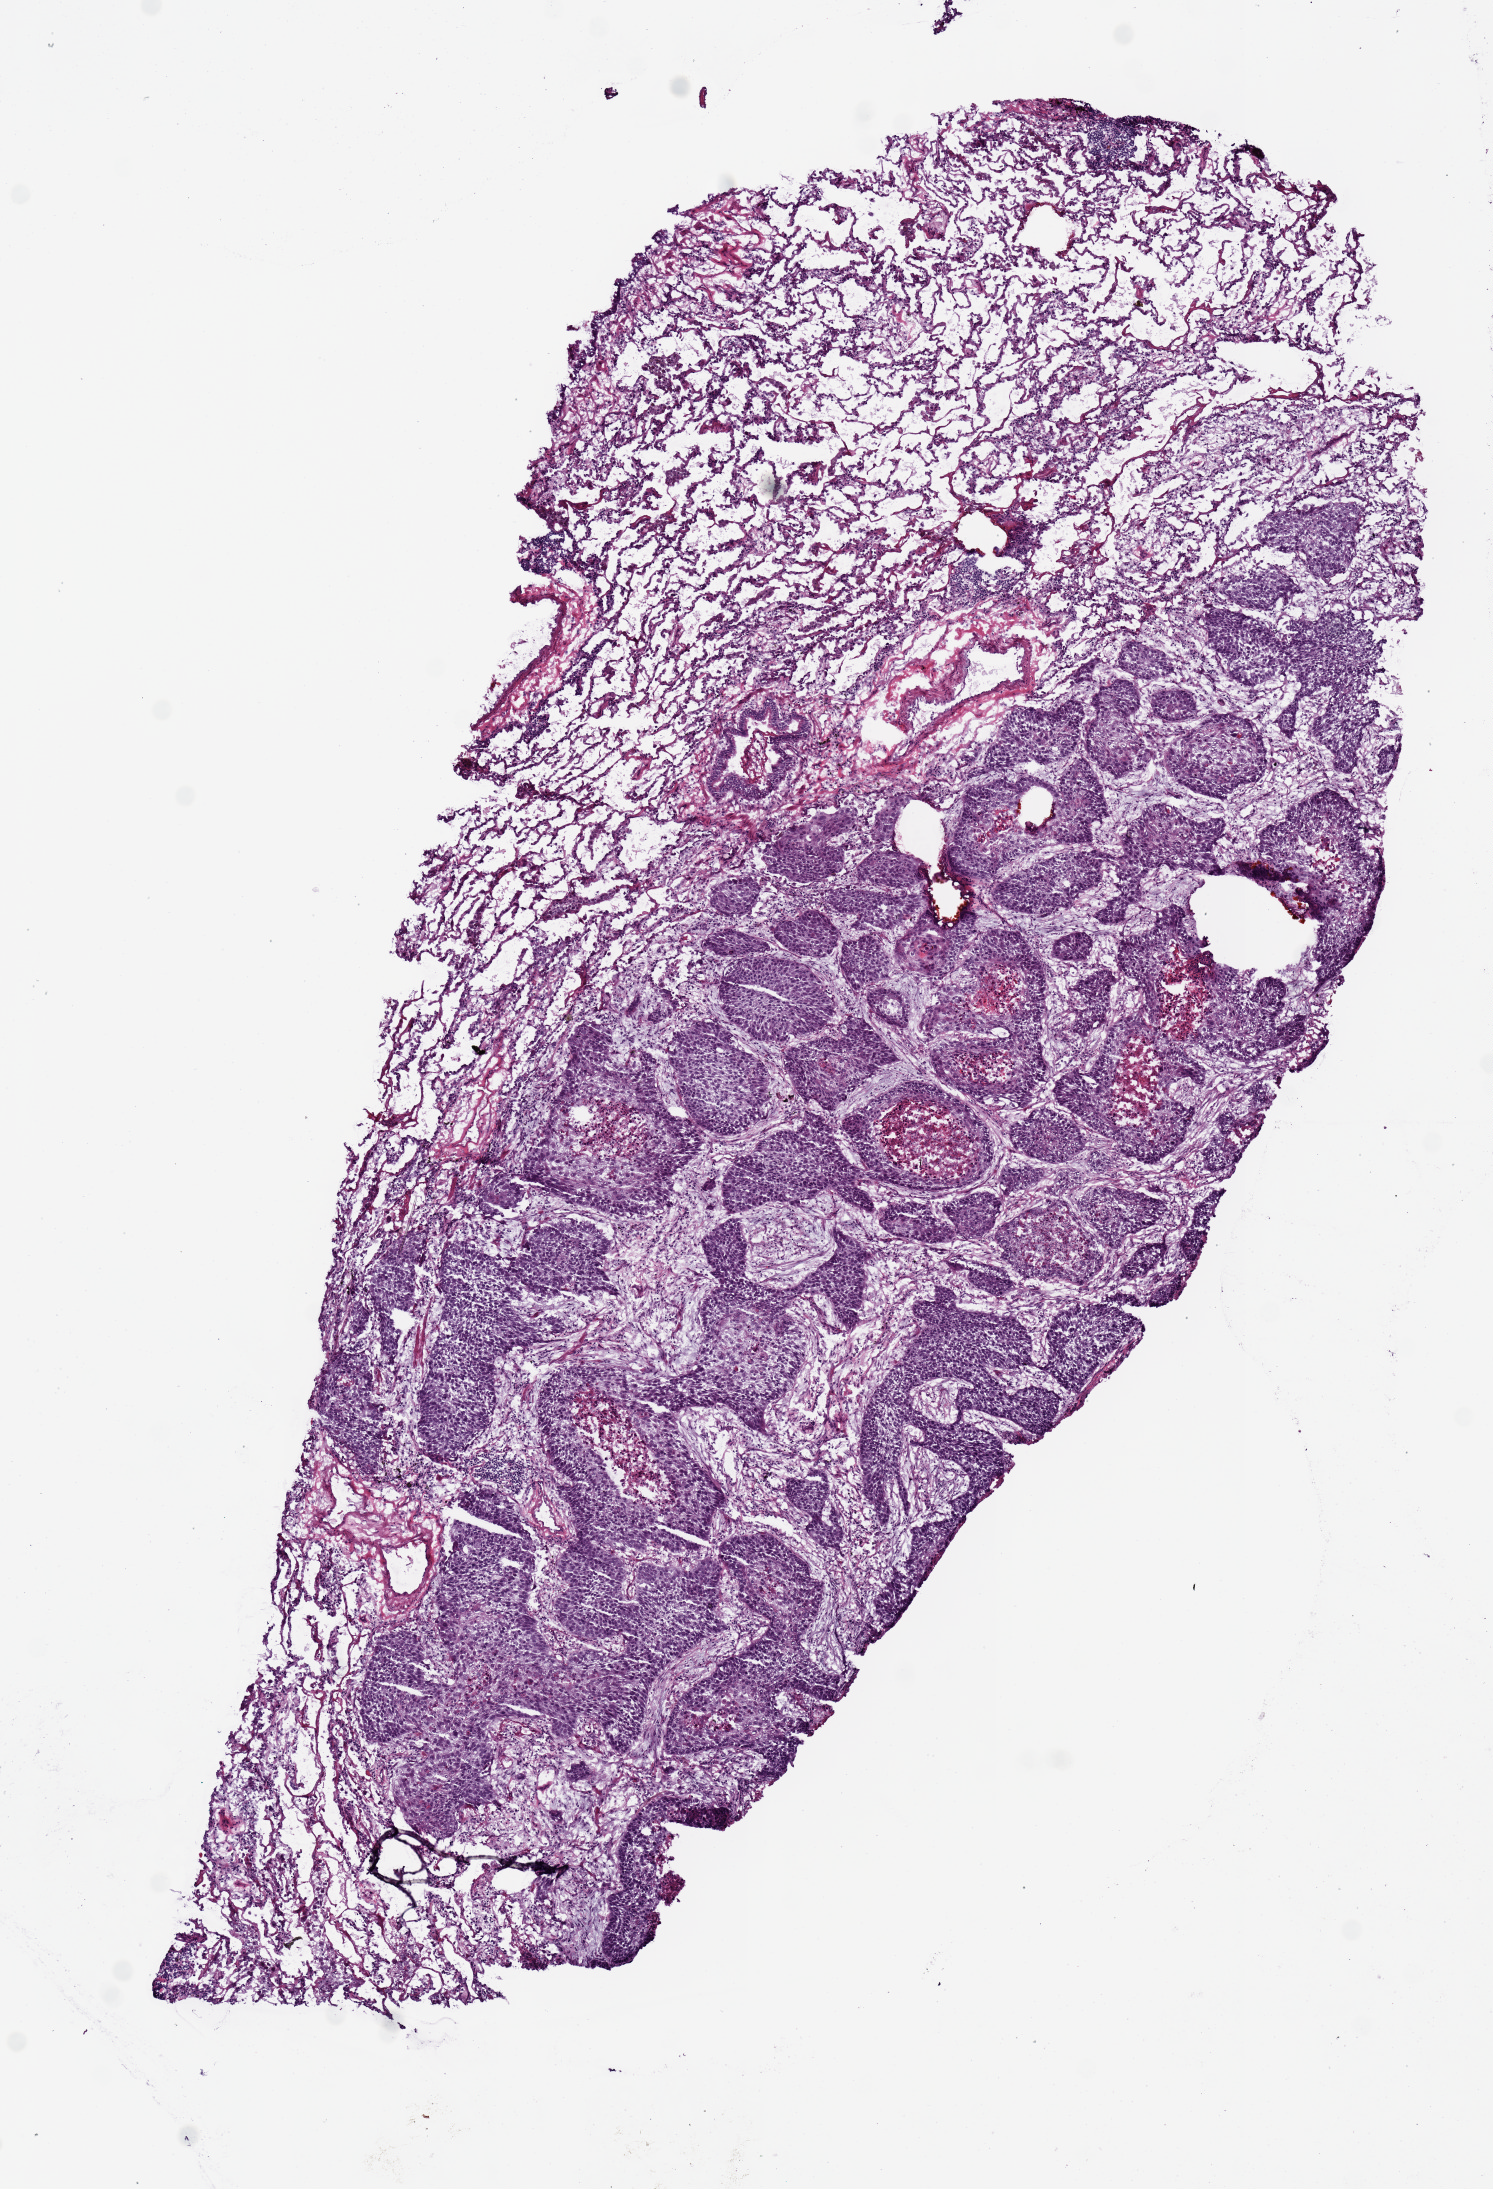
Digitized H&E tissue section (whole slide) — whole scanned area (about 5.9 x 8.7 mm, slide scanned at 20x) shown as a low-resolution overview; frozen section; sample: primary tumour, lung. Male patient; age at initial diagnosis 72 years. Pathologist review of this section (percent, as recorded): tumour cells 88%, tumour nuclei 70%, normal cells 0%, stromal cells 12%, necrosis 0%.
- TNM: T2a N0 M0
- pathologic diagnosis: Squamous cell carcinoma, NOS (upper lobe, lung)
- AJCC pathologic stage: IB (7th edition)